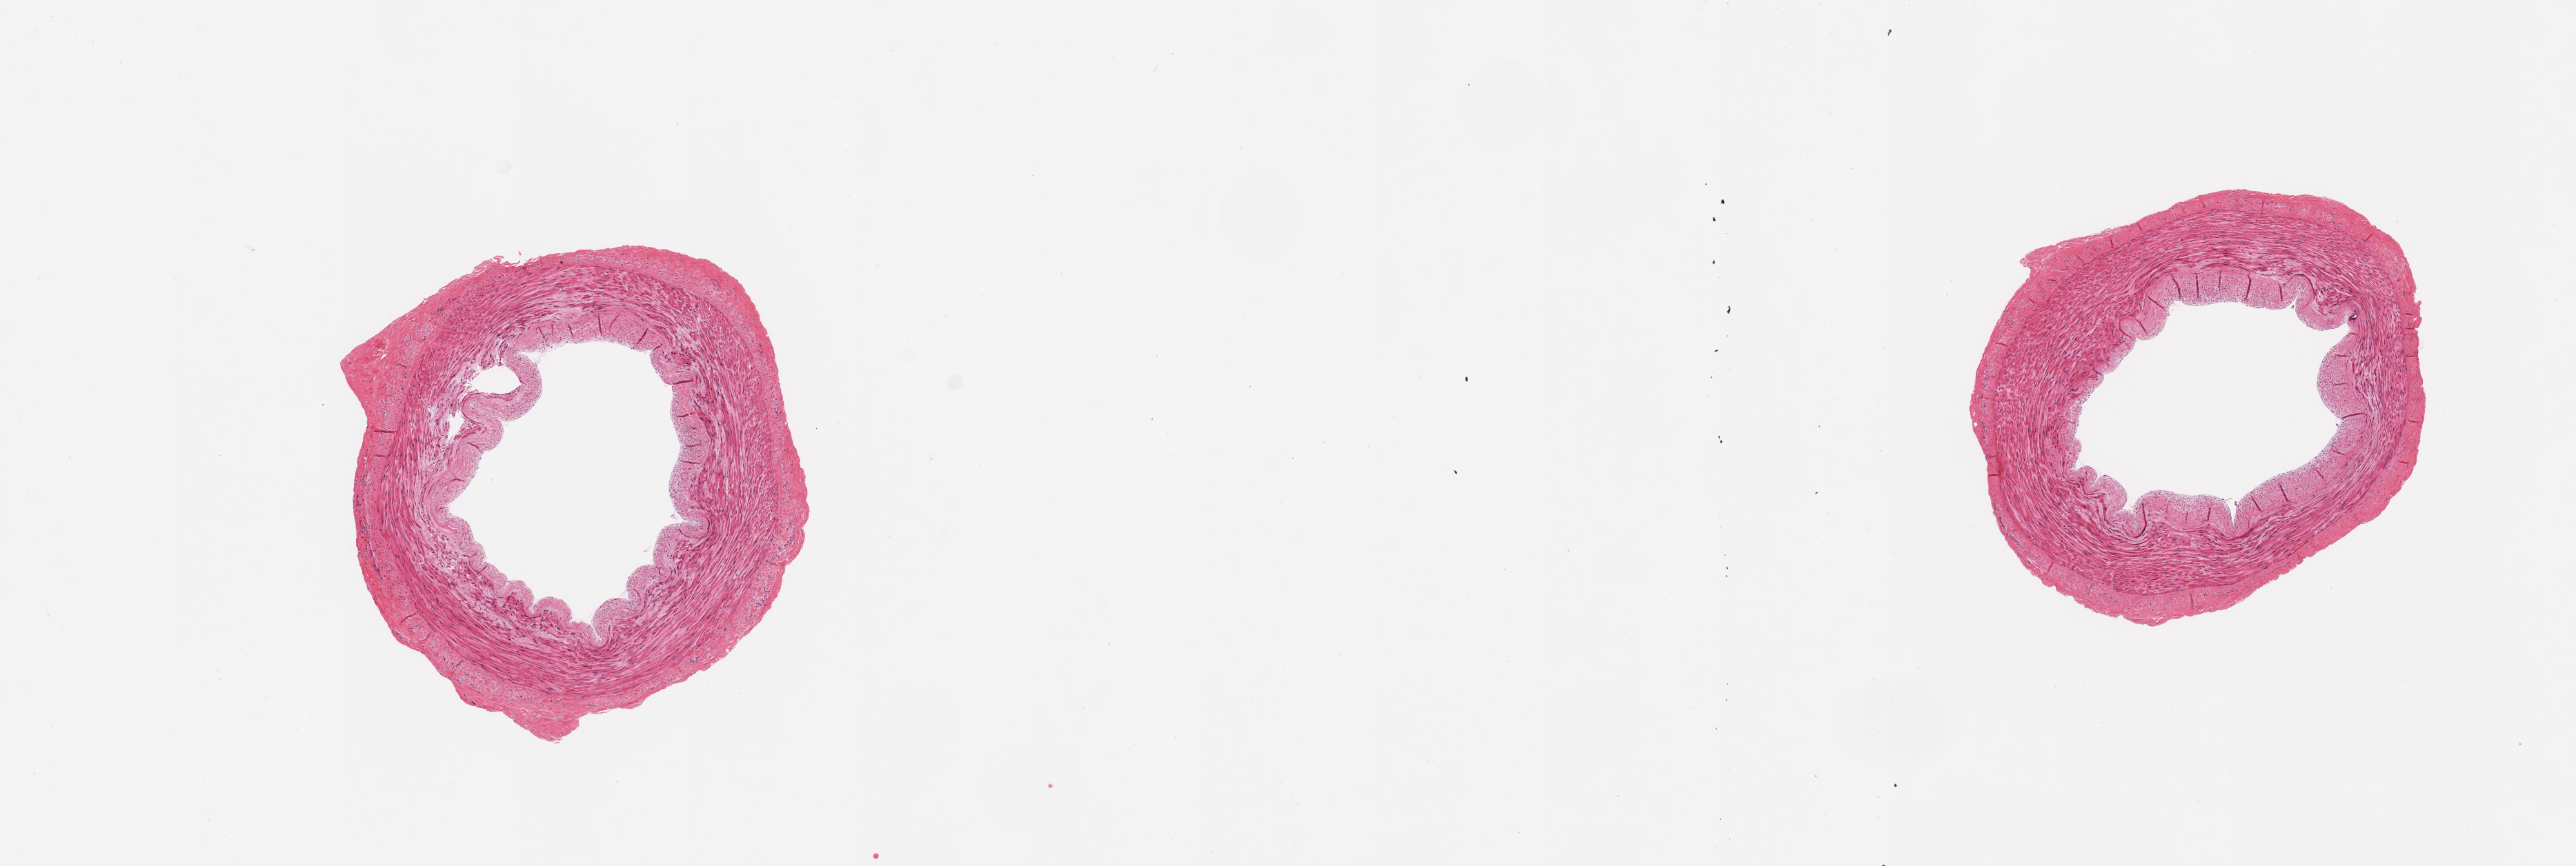
H&E whole-slide image, a low-resolution overview of the entire scanned area, about 14.8 x 5.0 mm (from a 20x scan); PAXgene-fixed, paraffin-embedded tissue; target tissue: tibial artery; tissue donor sample. Donor sex: male.
Pathologist's review note for this sample: 2 pieces; well trimmed, some intimal thickening, mild plaque.